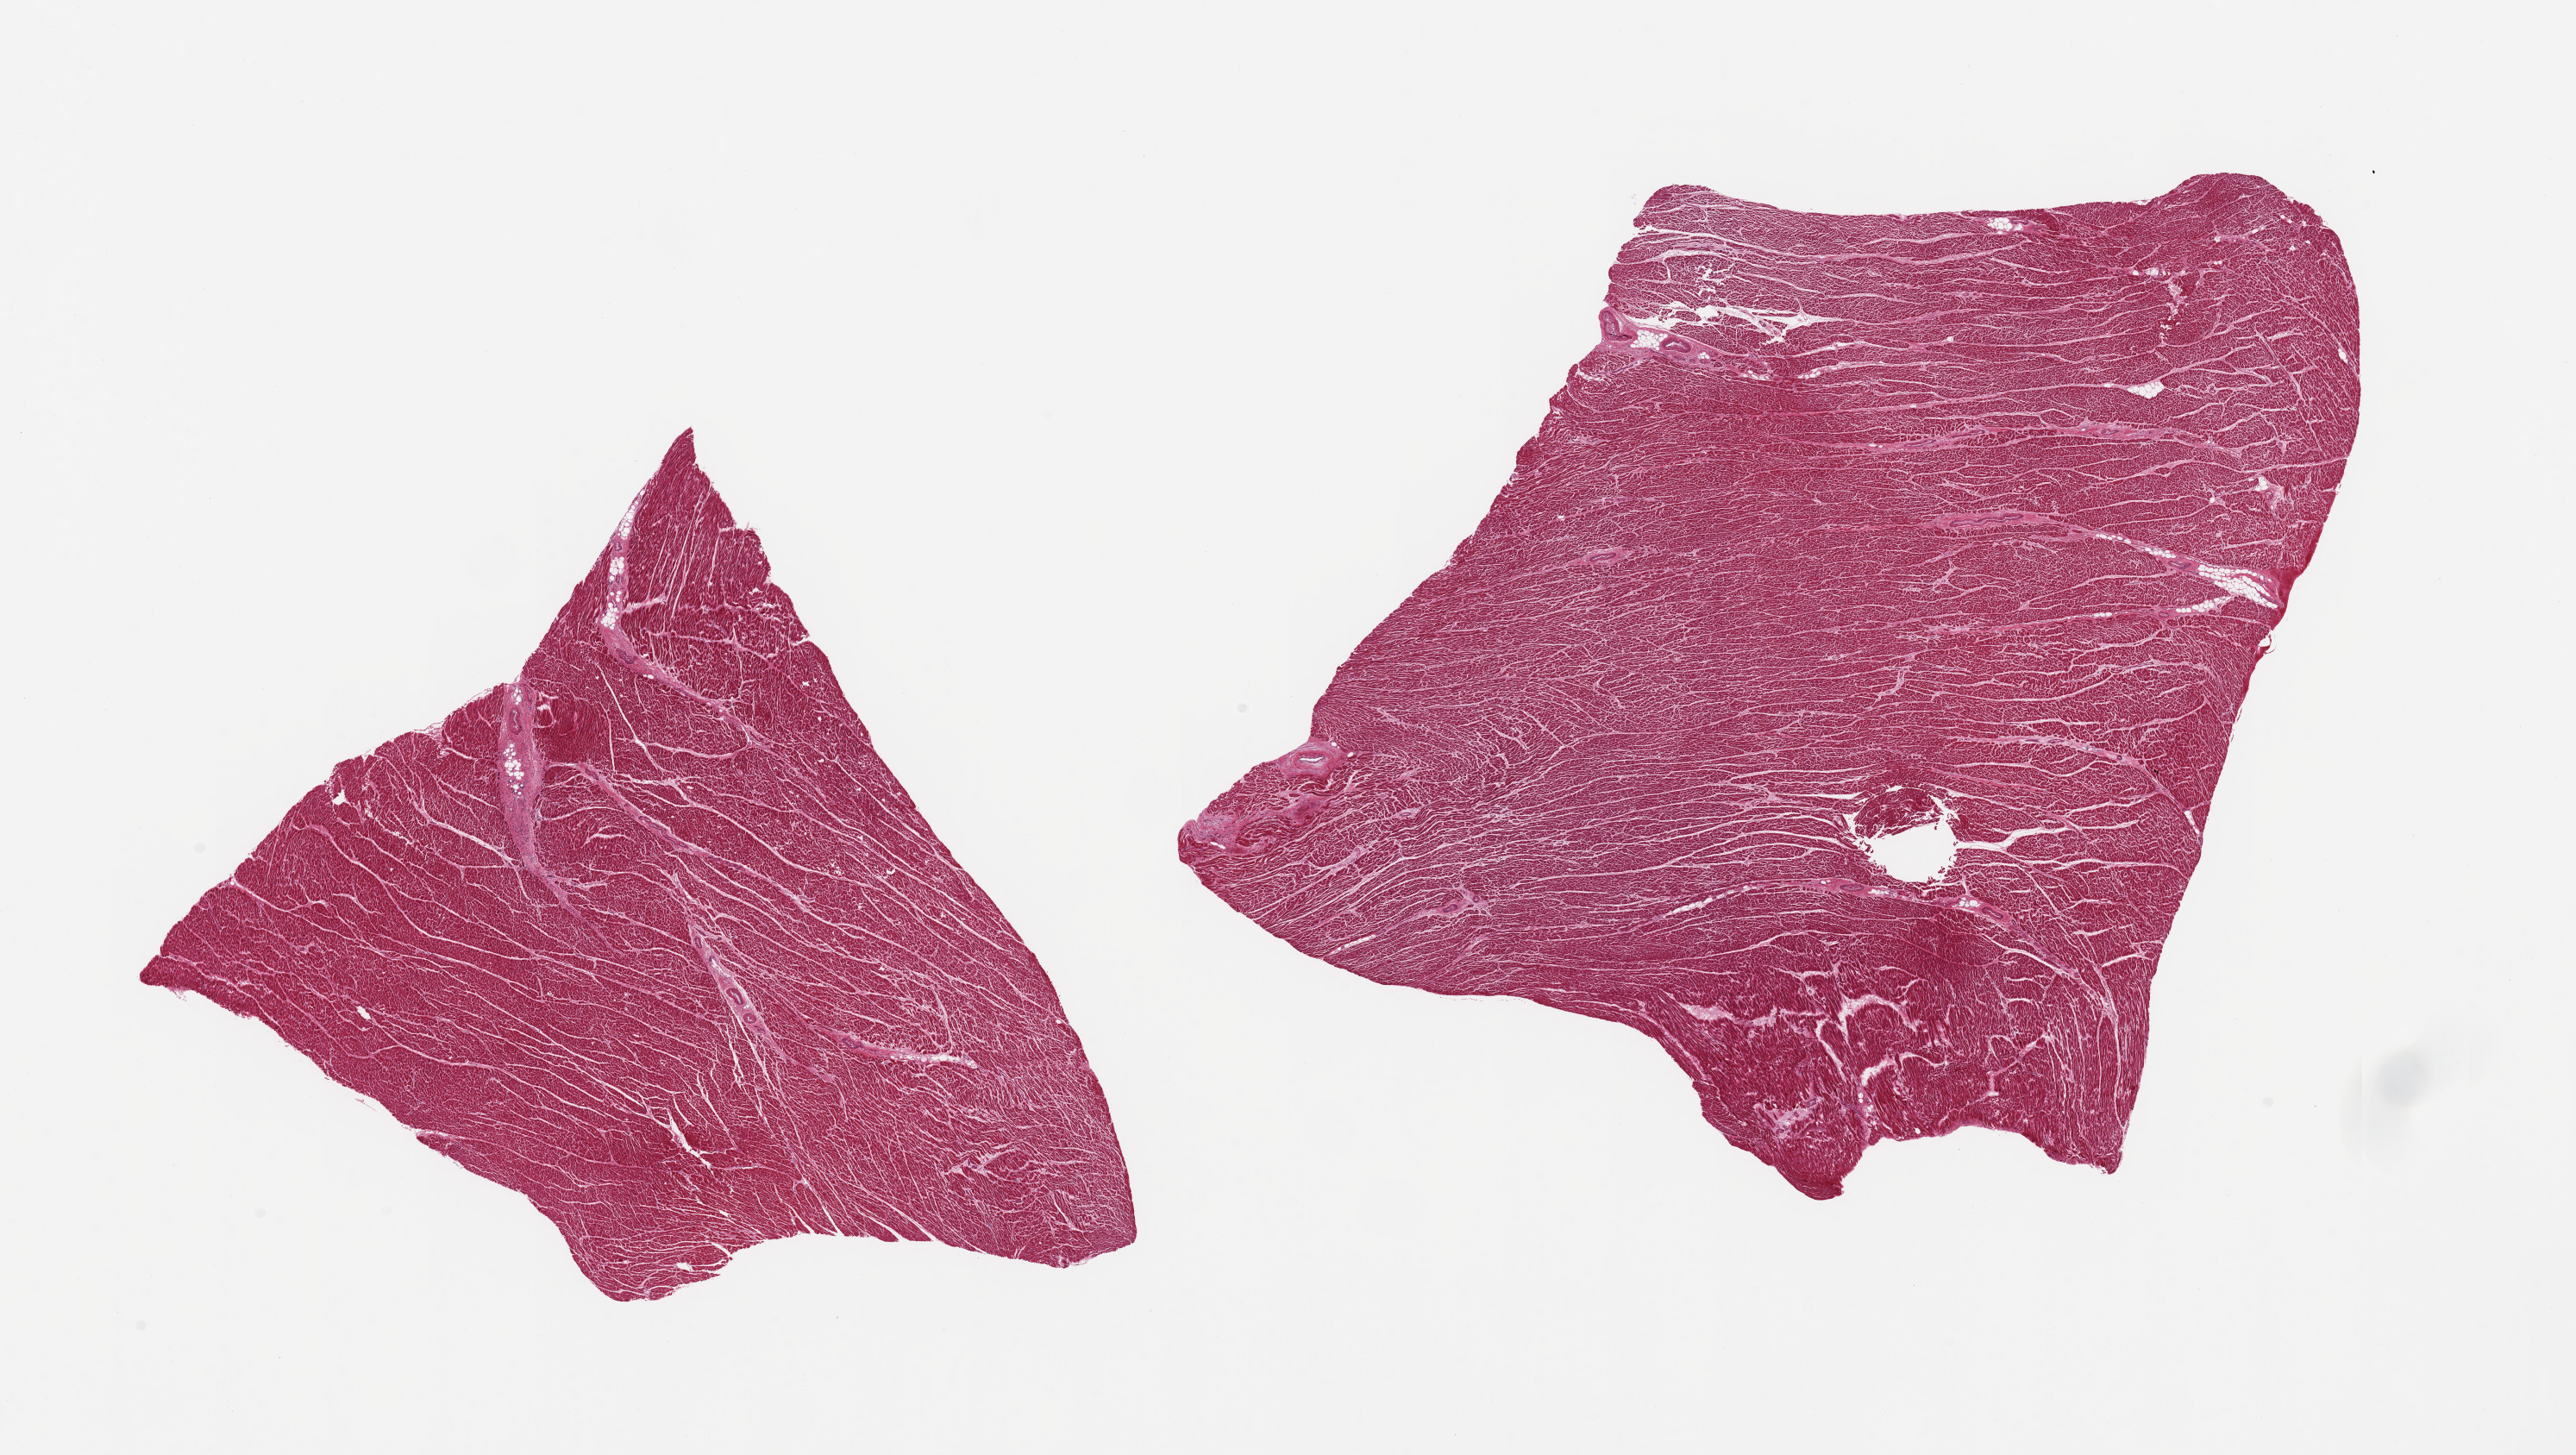
Whole-slide image, hematoxylin and eosin (H&E) stain, brightfield — whole scanned area (about 23.6 x 13.3 mm) shown as a low-resolution overview; PAXgene-fixed paraffin-embedded (PFPE) section; target tissue: heart; donor tissue sample. Female donor.
Reviewer comment on this tissue sample: 2 pieces, mild chronic ischemic changes/interstitial fibrosis.